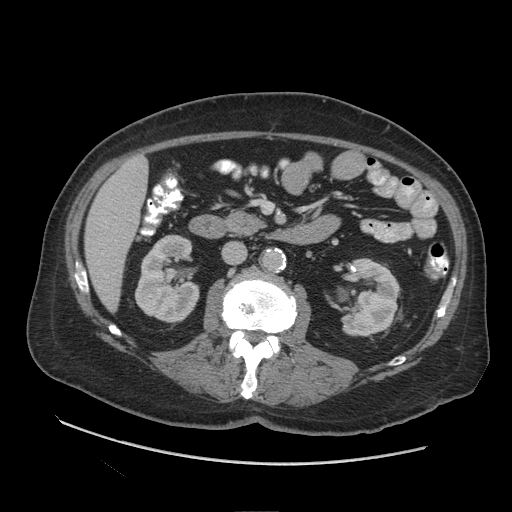
Contrast-enhanced abdominal CT (liver protocol), one axial slice; position 33 of 109 along the scan axis; reconstruction kernel STANDARD; 140 kVp; soft-tissue window (W 400 / L 40 HU); 2.5 mm slice thickness; 512 × 512 image matrix, field of view 420 × 420 mm. Case-level facts recorded for this patient, not image findings: diagnosis: hepatocellular carcinoma (patient treated with transarterial chemoembolisation; whether this scan precedes or follows treatment is not stated here); TNM stage (as recorded): Stage-I; Child-Pugh class: A; tumour nodularity: uninodular.
Annotated regions visible in this slice (semi-automatic segmentation, software-assisted and operator-edited):
- liver parenchyma outside the tumour (the mass and vessels are separate outlines, so this box may not span the whole liver): bounding box [x1, y1, x2, y2] px = [84, 156, 148, 312]
- liver vessels: [99, 227, 107, 288]